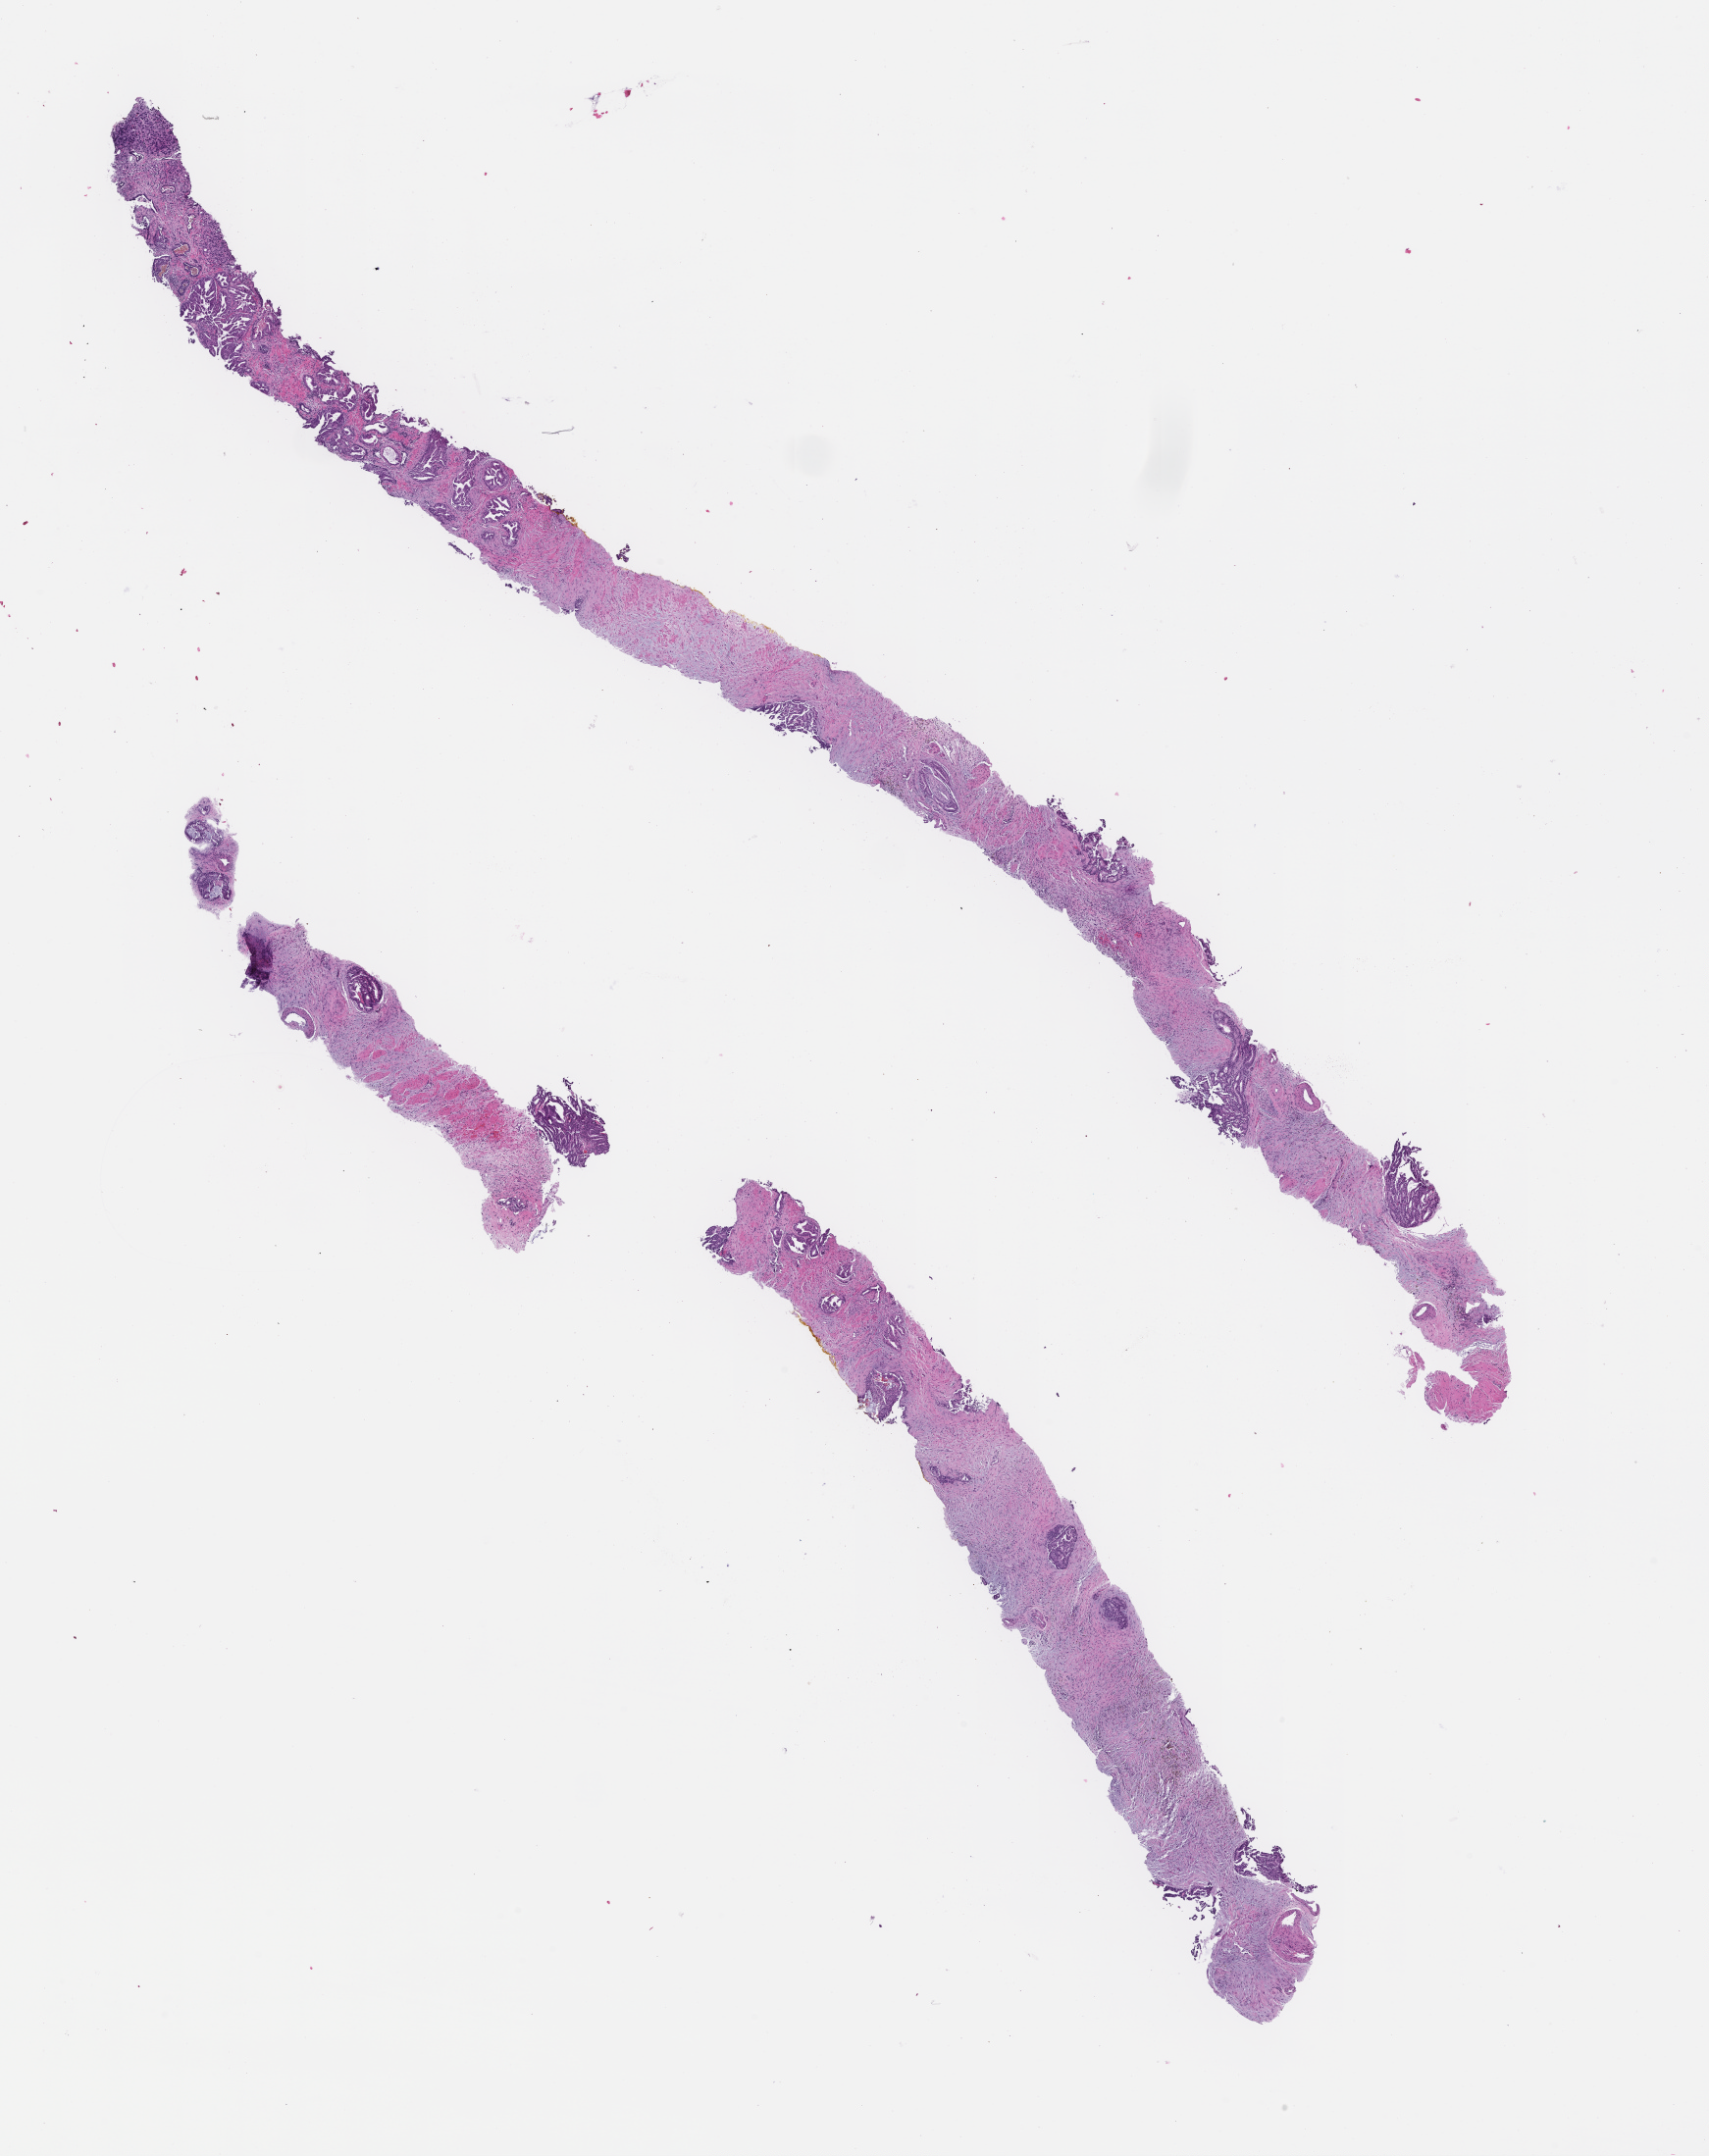
Digitized hematoxylin and eosin (H&E)-stained section, whole scanned area (about 14.1 x 17.8 mm) shown as a low-resolution overview. Formalin-fixed paraffin-embedded section. Tissue site: prostate. Specimen time point: archival tissue. Male patient.
• this section: primary tumour tissue
• diagnosis: Prostate Carcinoma